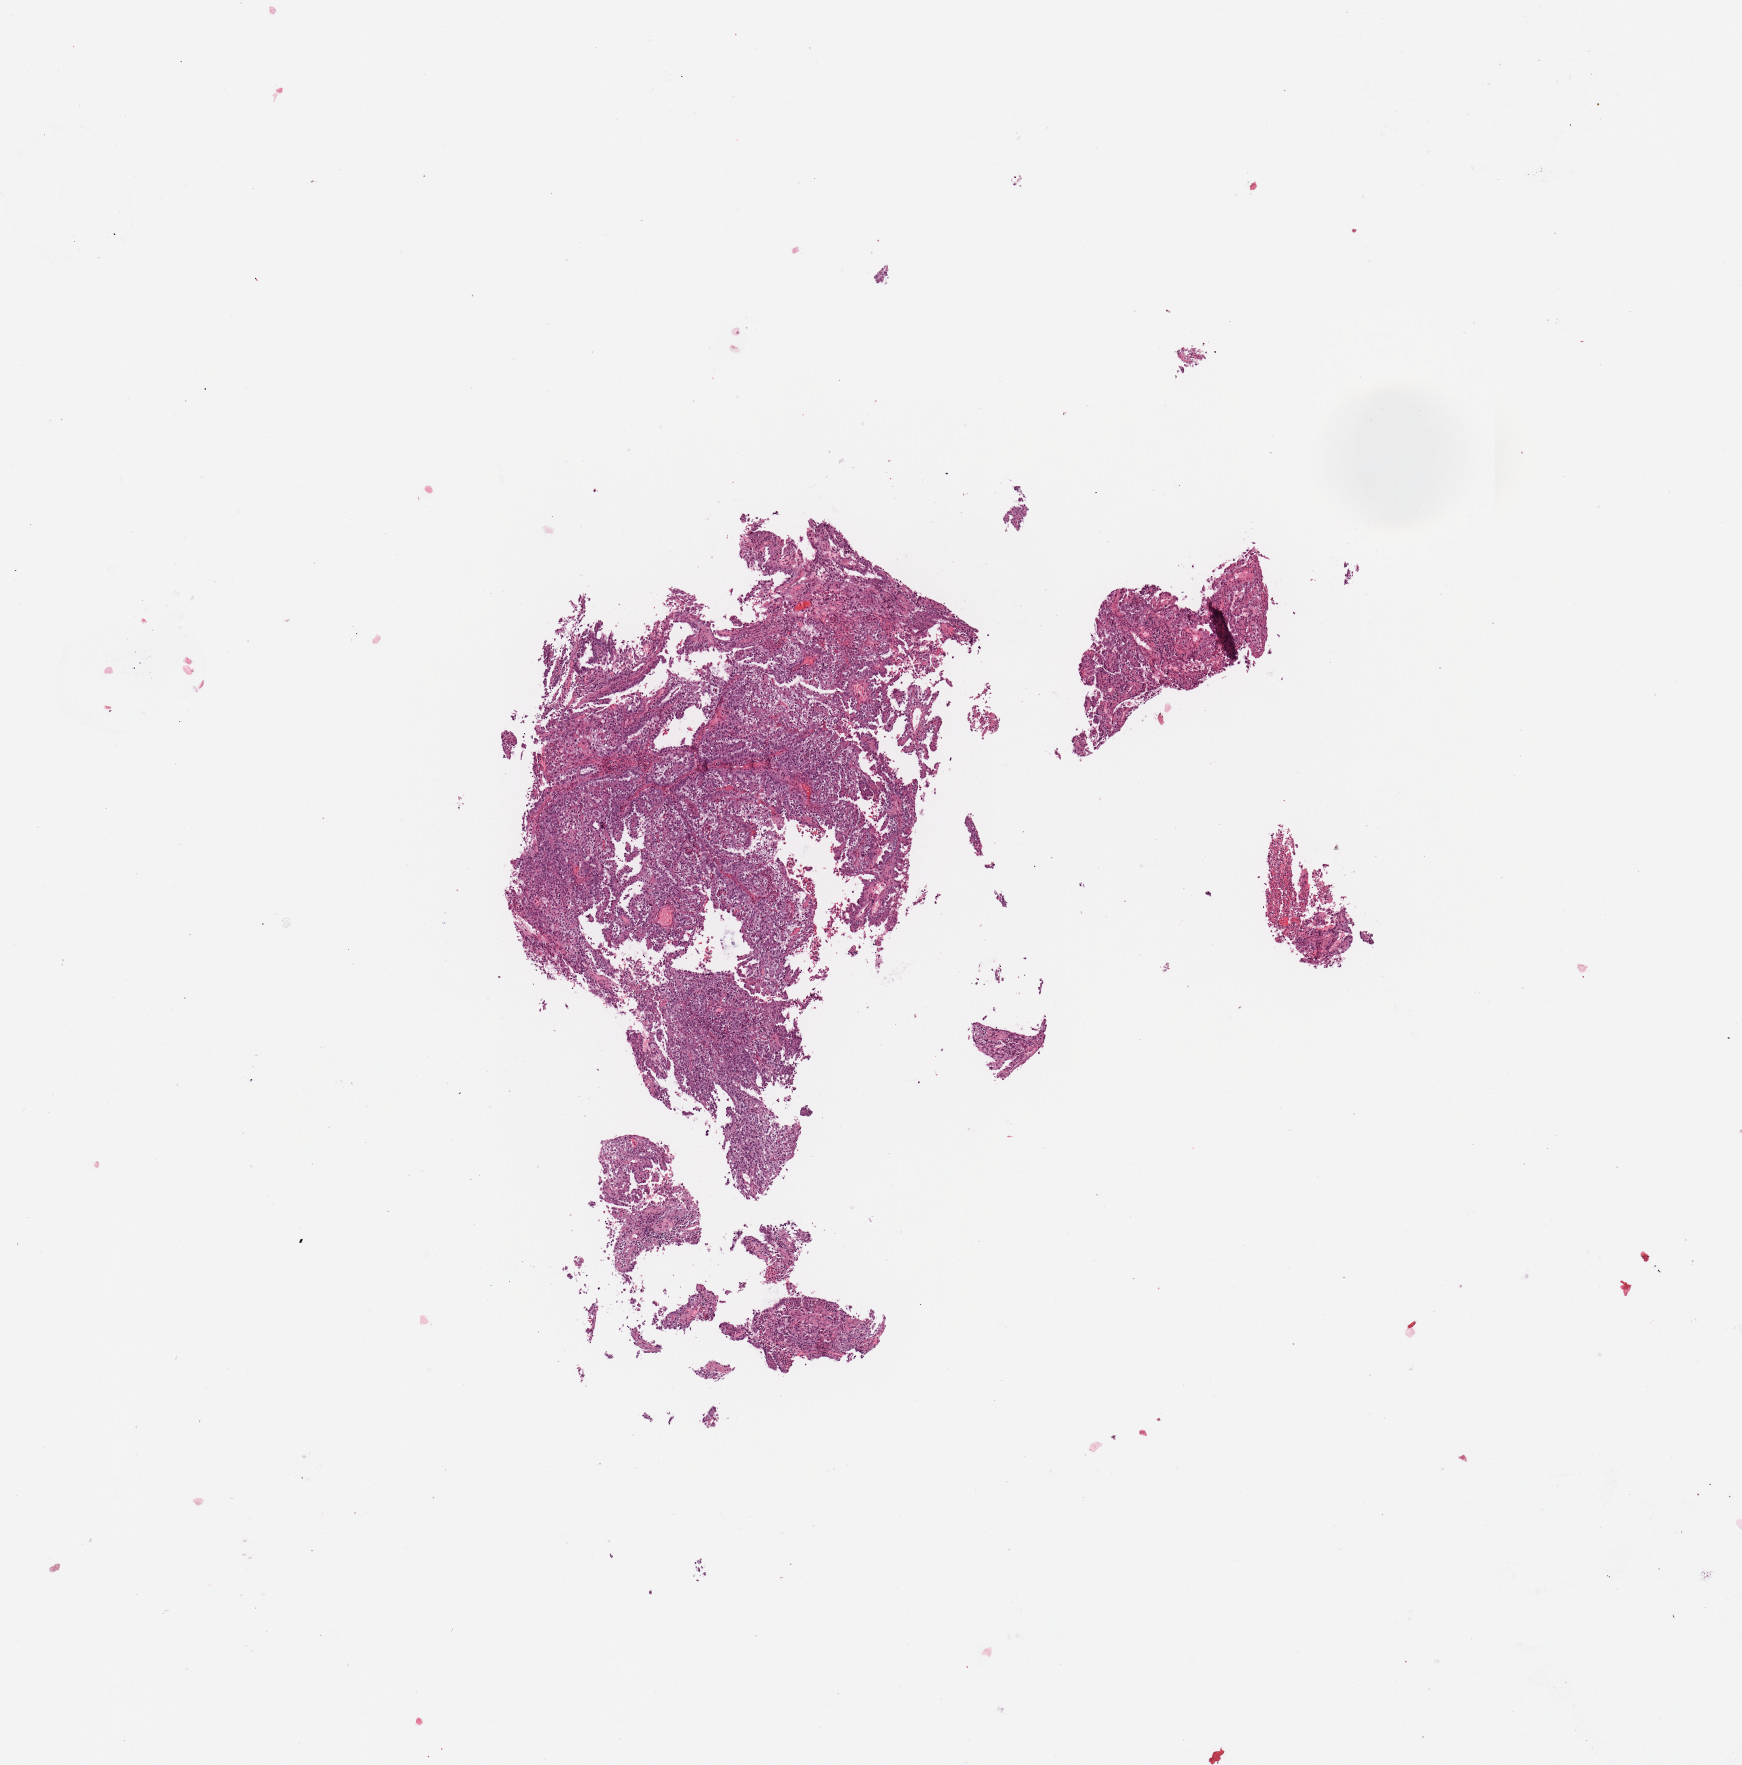
Digitized H&E-stained tissue section (whole slide), shown as a low-resolution overview of the whole scanned area (about 6.9 x 7.0 mm, from a 20x scan), tumour tissue sample, sampled site: uterus. 73-year-old female patient. Histologic grade: G2 (moderately differentiated). Composition of this section per pathologist review: tumour nuclei 95%, necrosis 0%.
Primary tumour site (as recorded): posterior endometrium. AJCC pathologic stage: IB. Histologic diagnosis: Endometrioid adenocarcinoma, NOS.